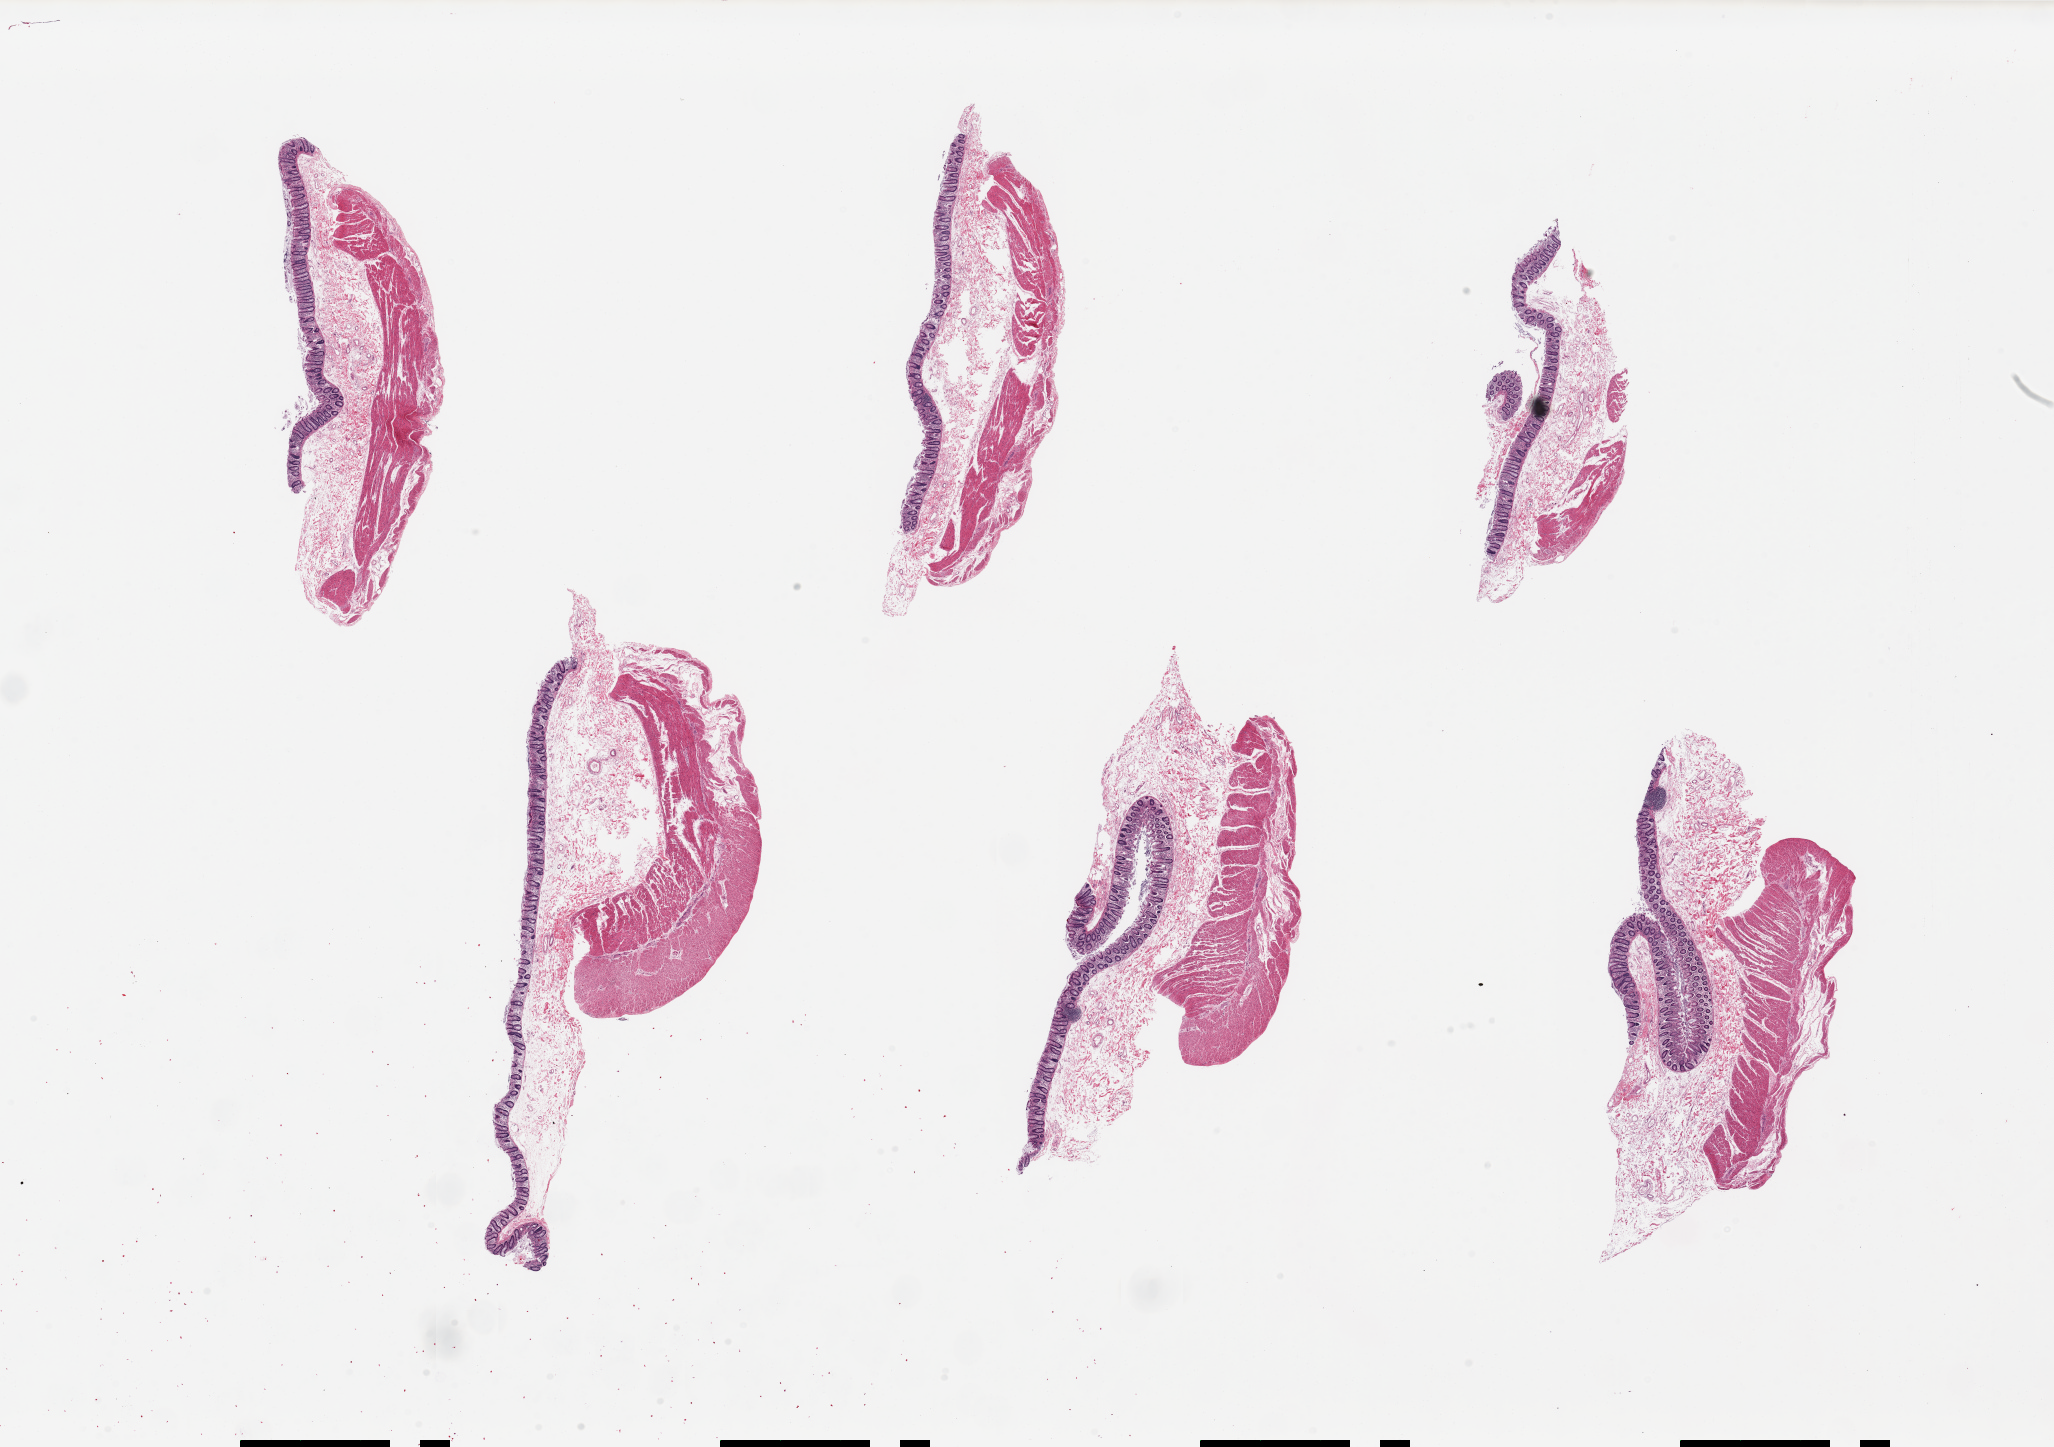
Hematoxylin and eosin (H&E) whole-slide image, brightfield — low-resolution overview of the scanned area, about 32.5 x 22.9 mm (acquisition: 20x scan), PAXgene-fixed, paraffin-embedded tissue, section of transverse colon (target tissue), donor tissue sample. Donor: male.
- review note (as recorded): 6 pieces, up to 11x4mm; Mucosa varies from mild to moderate autolysis. All pieces are well sampled: mucosa and muscularis